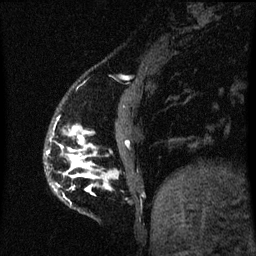
Breast MRI (dynamic contrast-enhanced), one sagittal slice. Slice 11 of 60 in the series (ordered by position). Dynamic contrast-enhanced series, image 2 of 3 at this slice position (ordered by acquisition). 1.5 T. TE 4.2 ms, TR 8 ms. 2 mm slice thickness. 256 × 256 image matrix, field of view 190 × 190 mm. Patient: female, 50 years.
Annotated regions visible in this slice (semi-automatic segmentation, software-assisted and operator-edited):
- analysis volume of interest (the breast-tissue region the enhancement analysis was run in; not a lesion): box from (x=50, y=126) to (x=91, y=191) px
- tumour enhancement mask (voxels above the 70 % enhancement threshold inside the analysis volume of interest): (x=58, y=126)–(x=90, y=191)